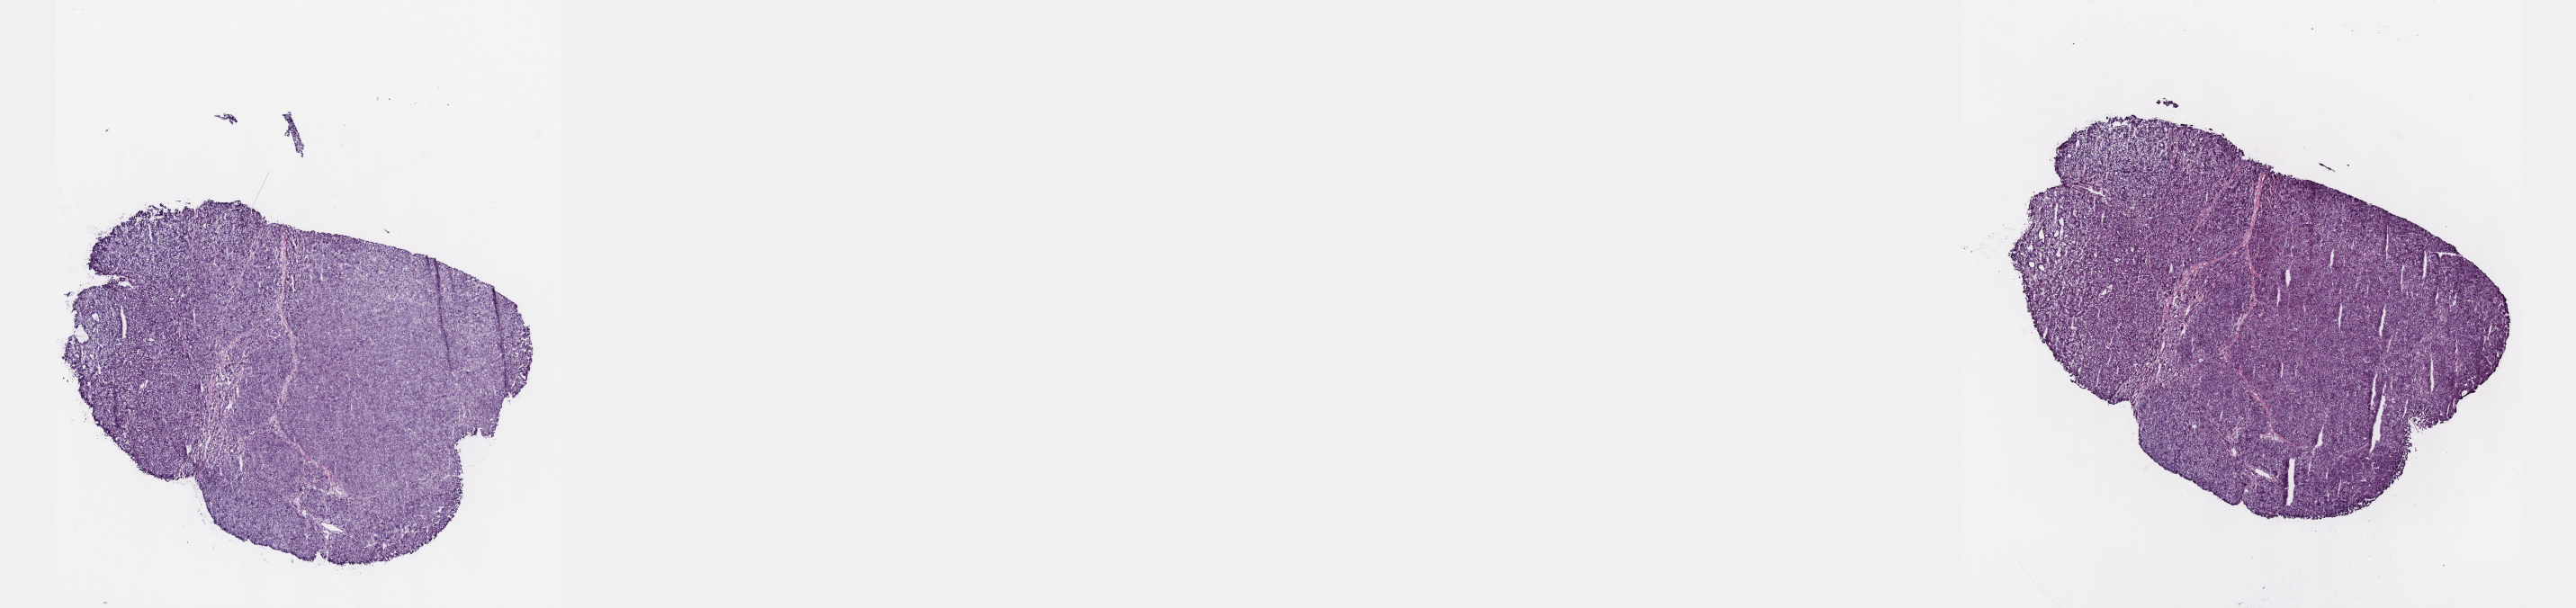
Digitized H&E-stained tissue section (whole slide) — shown as a low-resolution overview of the whole scanned area (about 23.1 x 5.5 mm), frozen section from the top of the tissue portion, sample: primary tumour, liver. Male patient; age at initial diagnosis 55 years. Histologic grade: G4 (undifferentiated). Composition of this section per pathologist review: tumour cells 100%, tumour nuclei 80%, normal cells 0%, stromal cells 0%, necrosis 0%. Infiltration values recorded for this section: lymphocyte infiltration 2%, monocyte infiltration 0%, neutrophil infiltration 0%.
TNM: T1 N0 M0. AJCC pathologic stage: I (7th edition). Histologic diagnosis: Hepatocellular carcinoma, NOS.